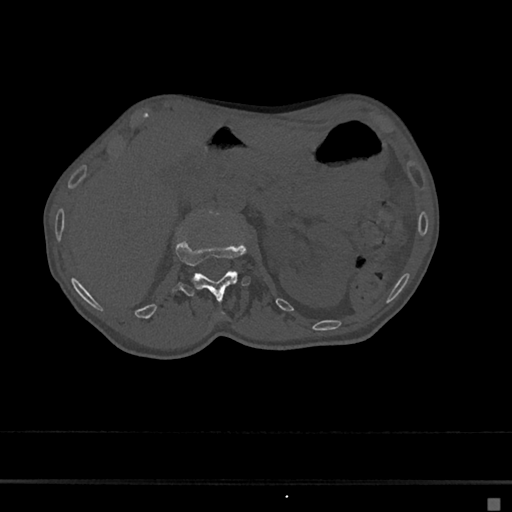
CT including the spine, one axial slice; position 65 of 797 along the scan axis; reconstruction kernel Br40s/3; 120 kVp; bone window (W 1800 / L 400 HU); 0.5 mm slice thickness; 512 × 512 image matrix, field of view 360 × 360 mm. Patient: female, 68 years. Case-level facts recorded for this patient, not image findings: primary cancer: renal.
Outlined on this slice (semi-automatic segmentation, software-assisted and operator-edited):
- L1 vertebra: bounding box <172,237,261,300> (left, top, right, bottom; pixels)